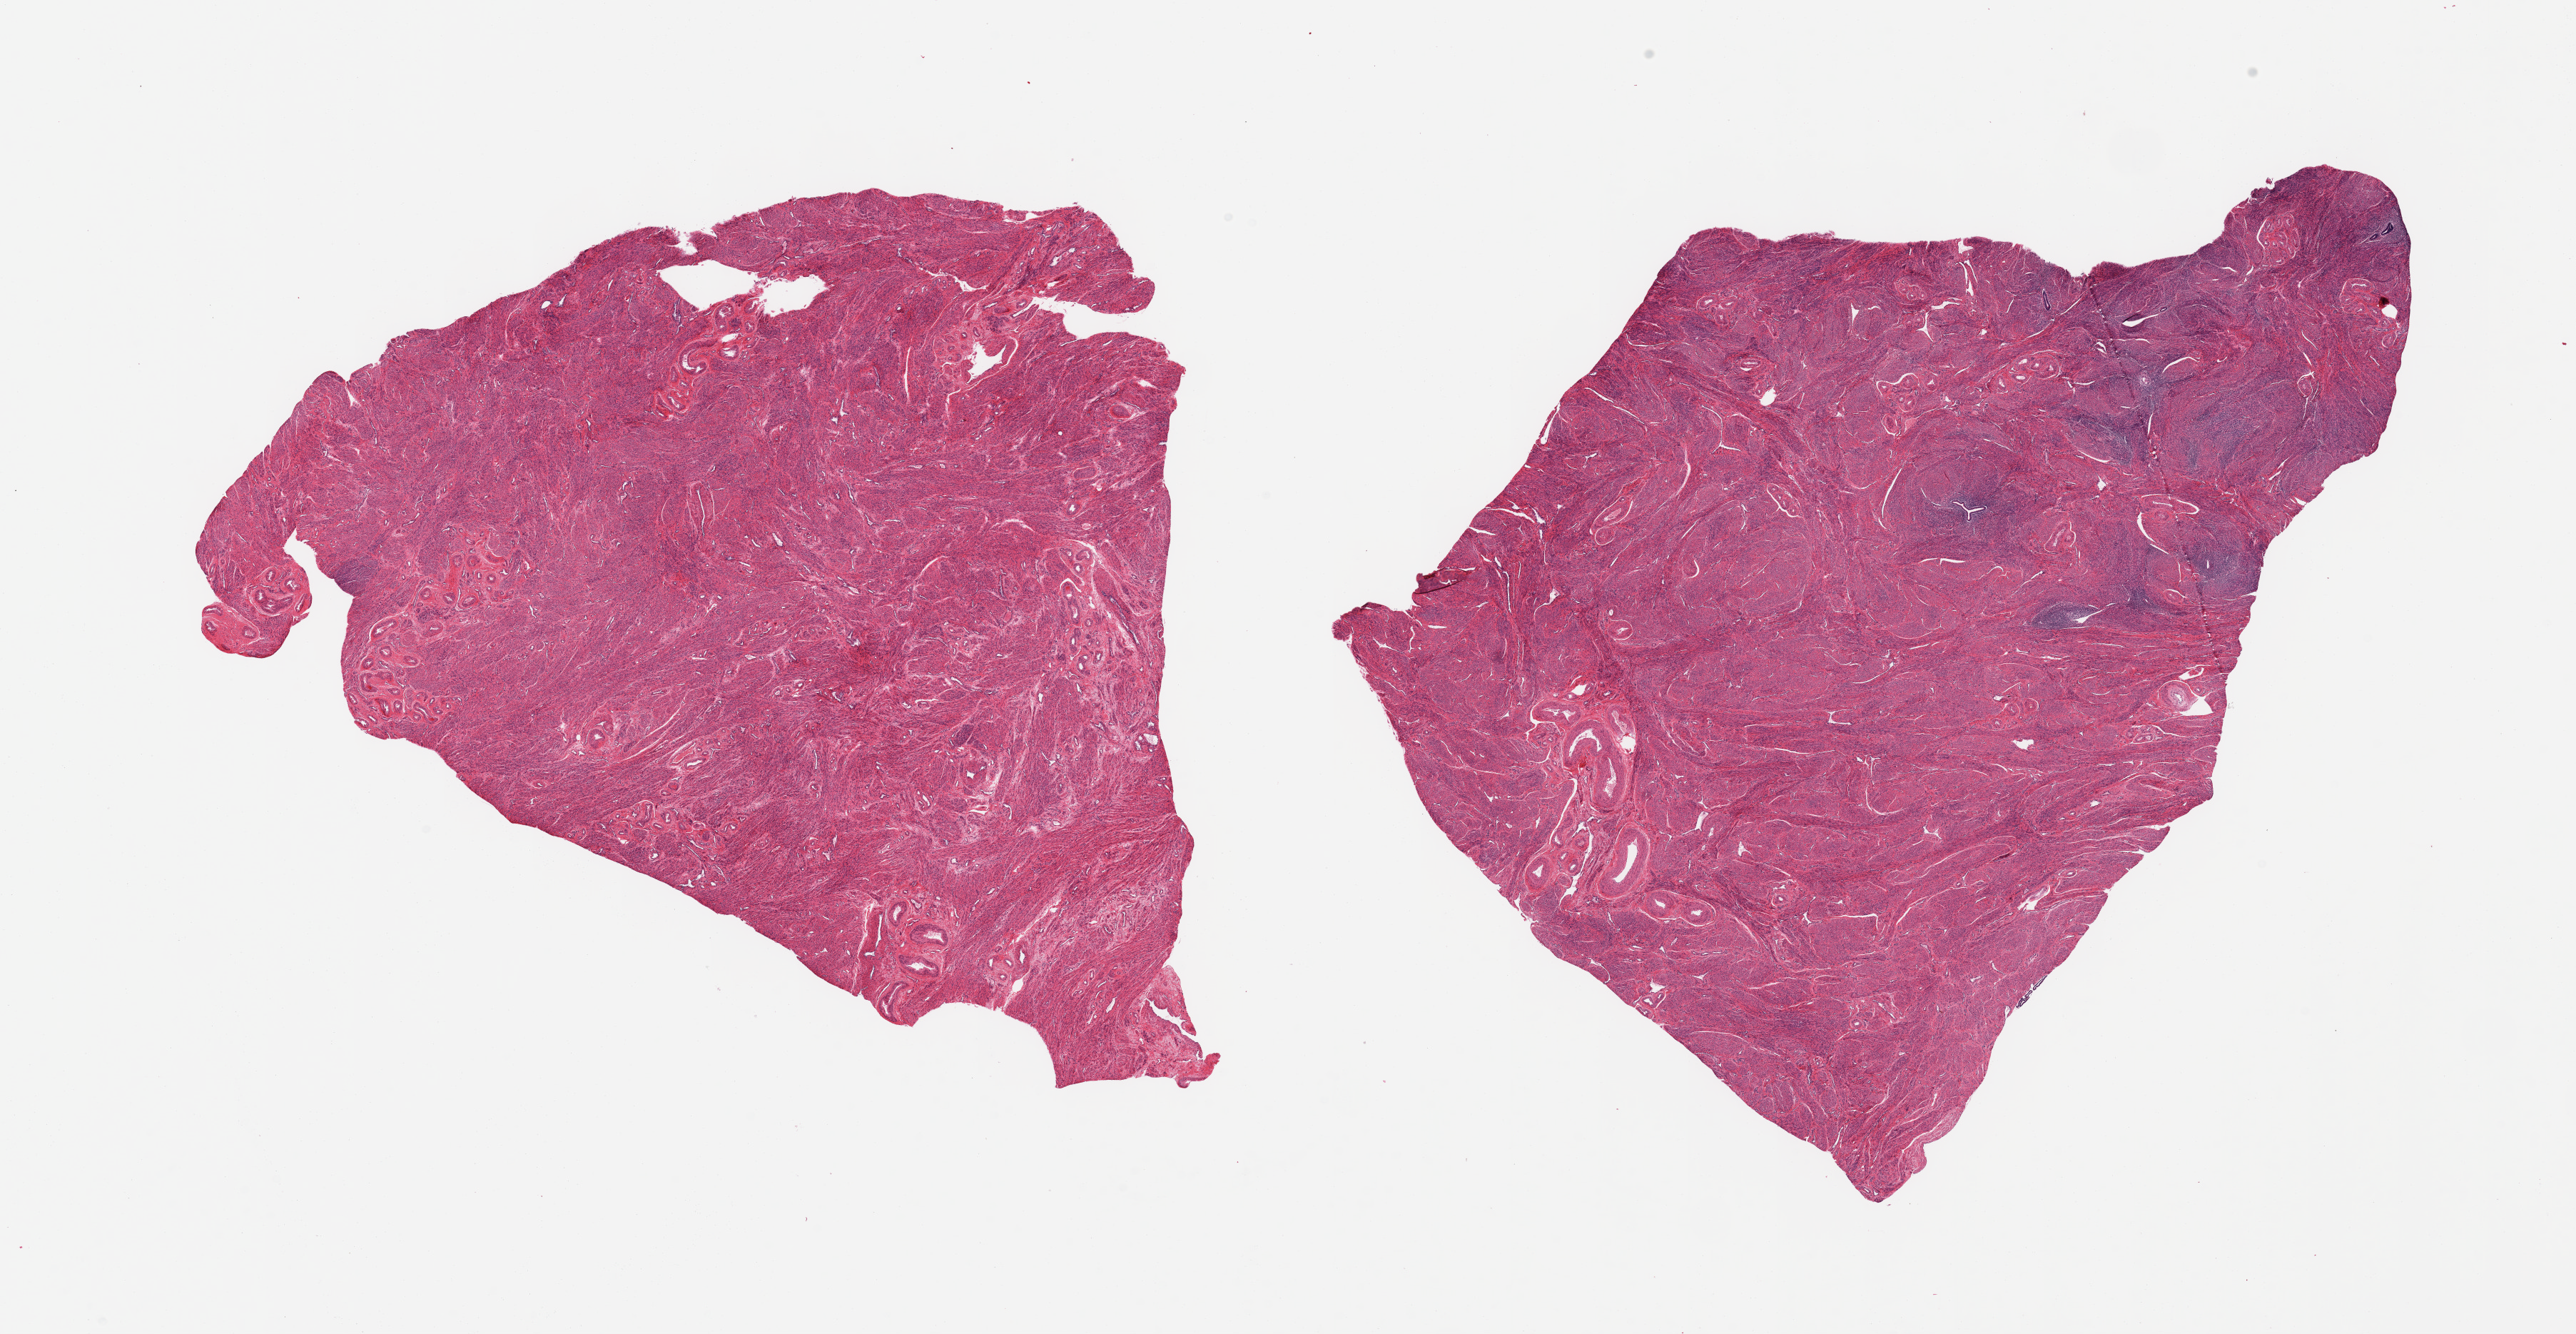
Whole-slide image, hematoxylin and eosin (H&E) stain — shown as a low-resolution overview of the whole scanned area (about 28.5 x 14.8 mm), PAXgene-fixed paraffin-embedded (PFPE) section, sampled site (target tissue): uterus, tissue donor sample.
• review note (as recorded): 2 pieces; atrophic endometrium in 1 piece with myometrial predominance; myometrium only in other piece (in this cut)